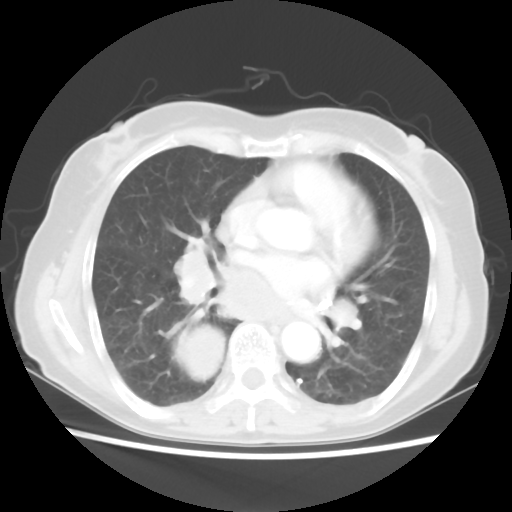
Chest CT, one axial slice. Slice 29 of 56 in the series (ordered by position). Reconstruction kernel STANDARD. 120 kVp. Lung window (W 1500 / L -600 HU). 5 mm slice thickness. 512 × 512 image matrix. Female patient, age 66 years. Case-level facts recorded for this patient, not image findings: clinical TNM (as recorded): T2 N3 M0; histopathological grade: G3.
Annotated regions visible in this slice (bounding box drawn by a radiologist):
- lung tumour (recorded histology: small cell carcinoma): bounding box (x1, y1, x2, y2) in pixels: (176, 317, 225, 381)